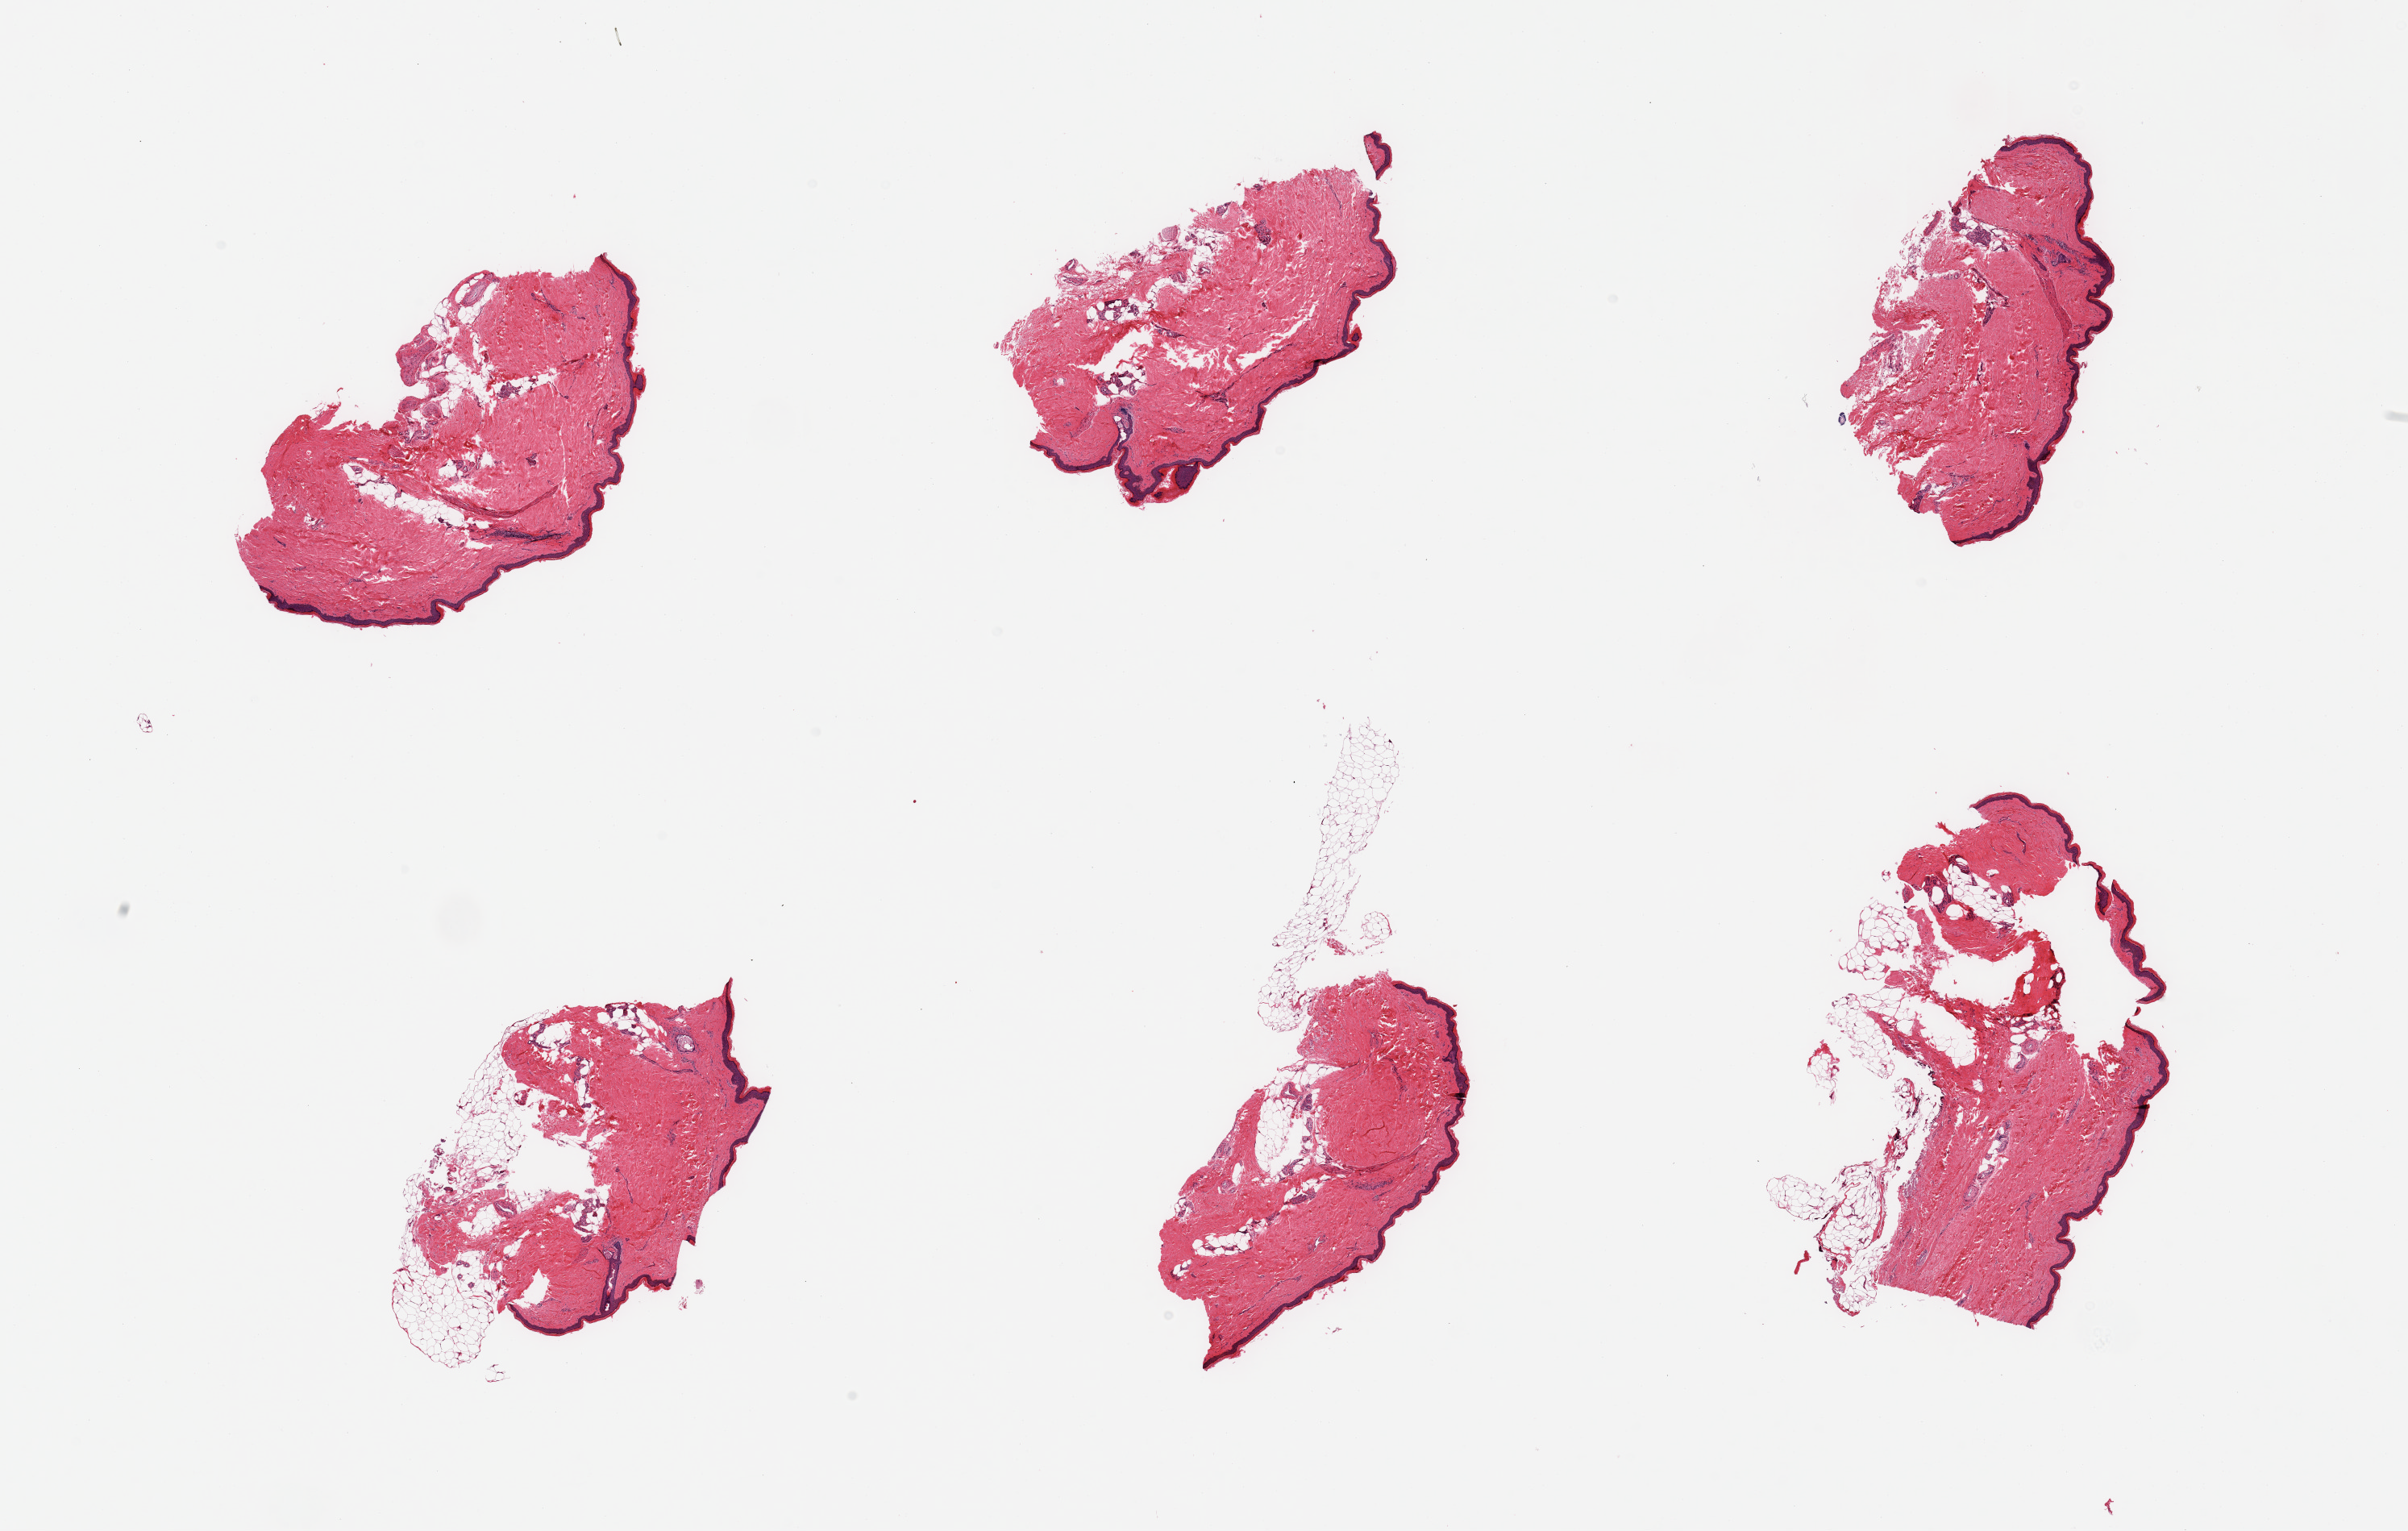
Whole-slide image, H&E stain, low-resolution overview of the scanned area, about 23.6 x 15.0 mm (from a 20x scan), PAXgene-fixed, paraffin-embedded tissue, section of skin of lower leg (target tissue), donor tissue sample. Female donor.
Review note (as recorded): 6 pieces; deep fat not trimmed on half pieces; 10% dermal fat.